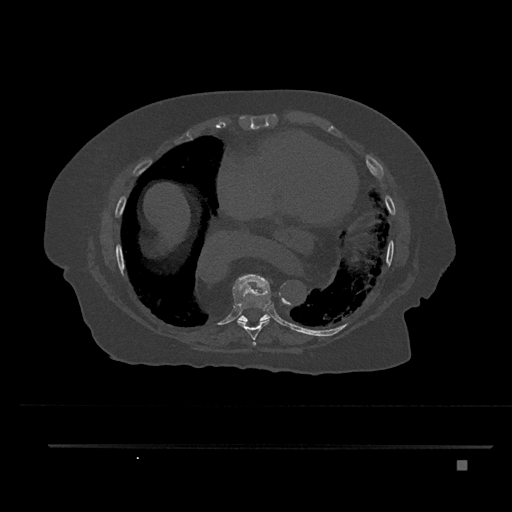
CT including the spine, one axial slice; reconstruction kernel Br40s/3; 120 kVp; bone window (W 1800 / L 400 HU); 0.5 mm slice thickness; 512 × 512 image matrix, field of view 437 × 437 mm. Patient: female, 76 years. From the clinical record (not read from this slice): primary cancer: lung; vertebrae with lytic lesions (as recorded): T11, L3.
Outlined on this slice (semi-automatically segmented with operator editing):
- T7 vertebra: box from (x=253, y=342) to (x=256, y=345) px
- T8 vertebra: (x=233, y=274)–(x=271, y=346)
- T9 vertebra: (x=237, y=311)–(x=271, y=322)